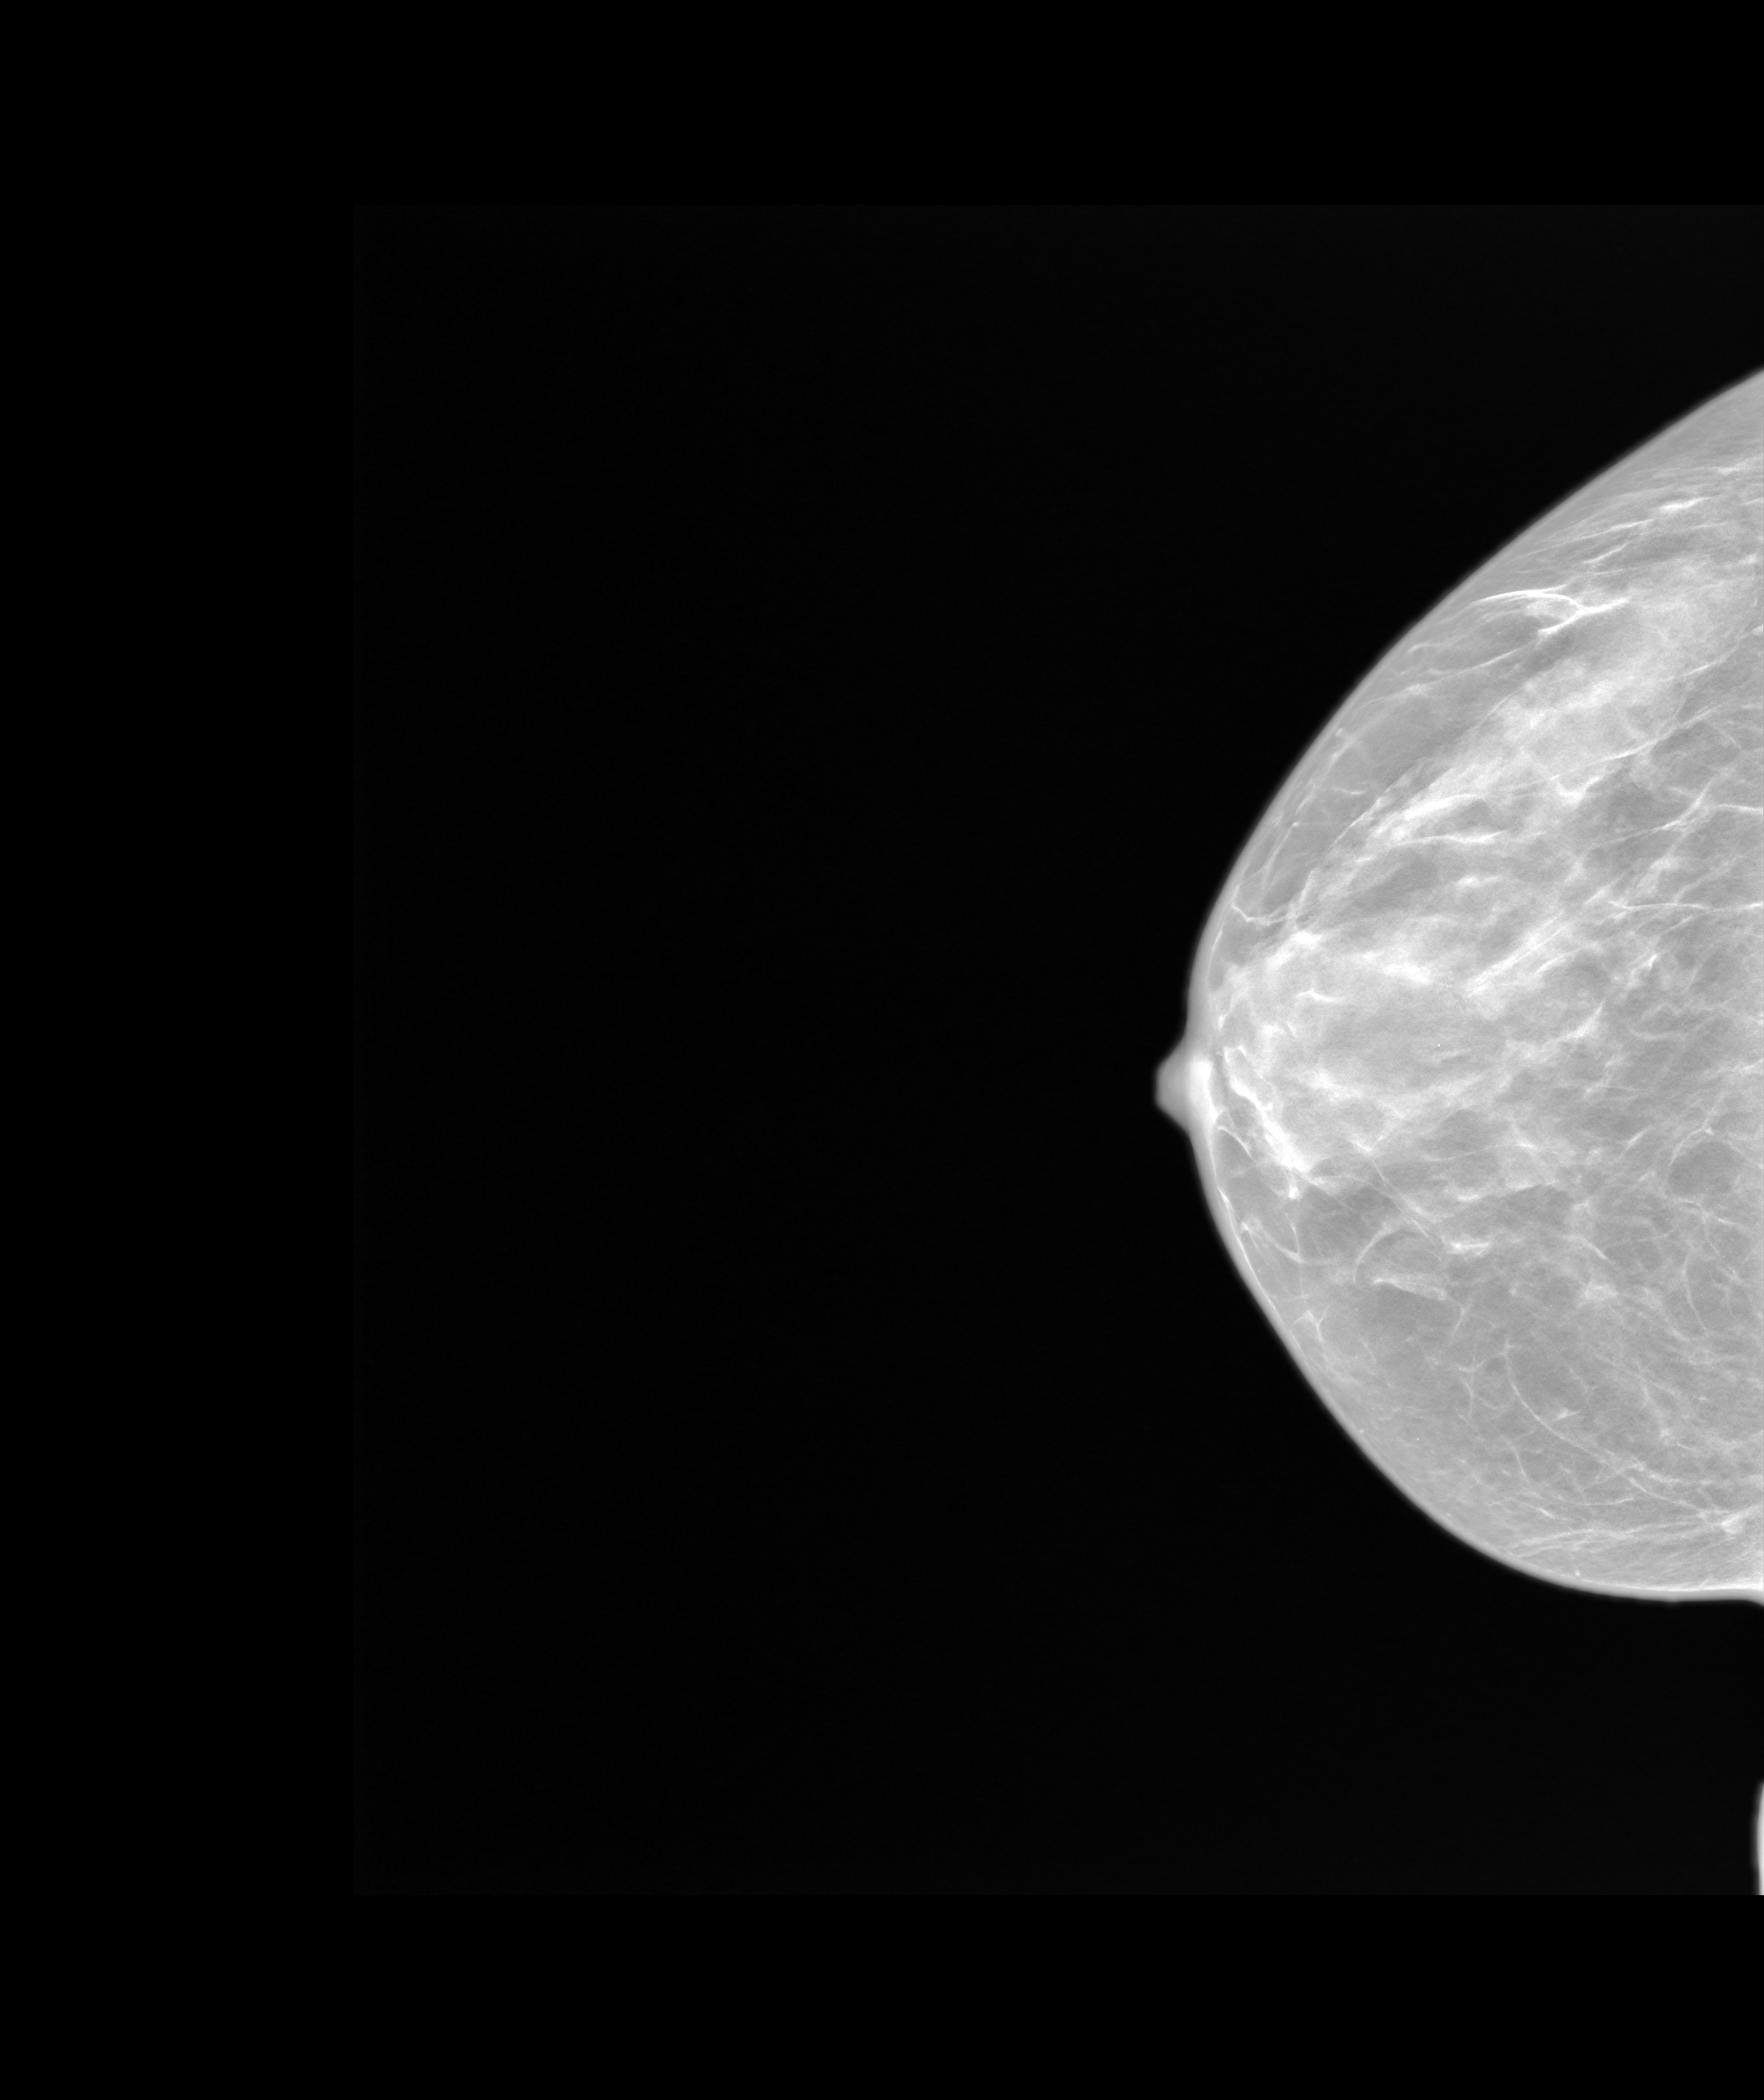
Screening examination, system: SenoIris_1SP1.2(425). Patient aged 49 years (female).
Image type: synthesized 2-D view from tomosynthesis. Breast: right. Projection: cranio-caudal projection.